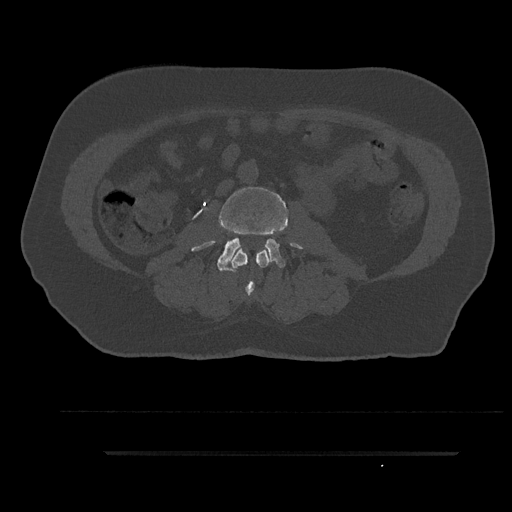
CT including the spine, one axial slice; reconstruction kernel Br40s/3; 120 kVp; bone window (W 1800 / L 400 HU); 512 × 512 image matrix, field of view 432 × 432 mm. Patient: male, 63 years. Case-level facts recorded for this patient, not image findings: primary cancer: renal; vertebrae with lytic lesions (as recorded): T8.
Annotated regions visible in this slice (semi-automatically segmented with operator editing):
- L2 vertebra: bounding box <232,250,269,297> (left, top, right, bottom; pixels)
- L3 vertebra: <192,185,302,271>